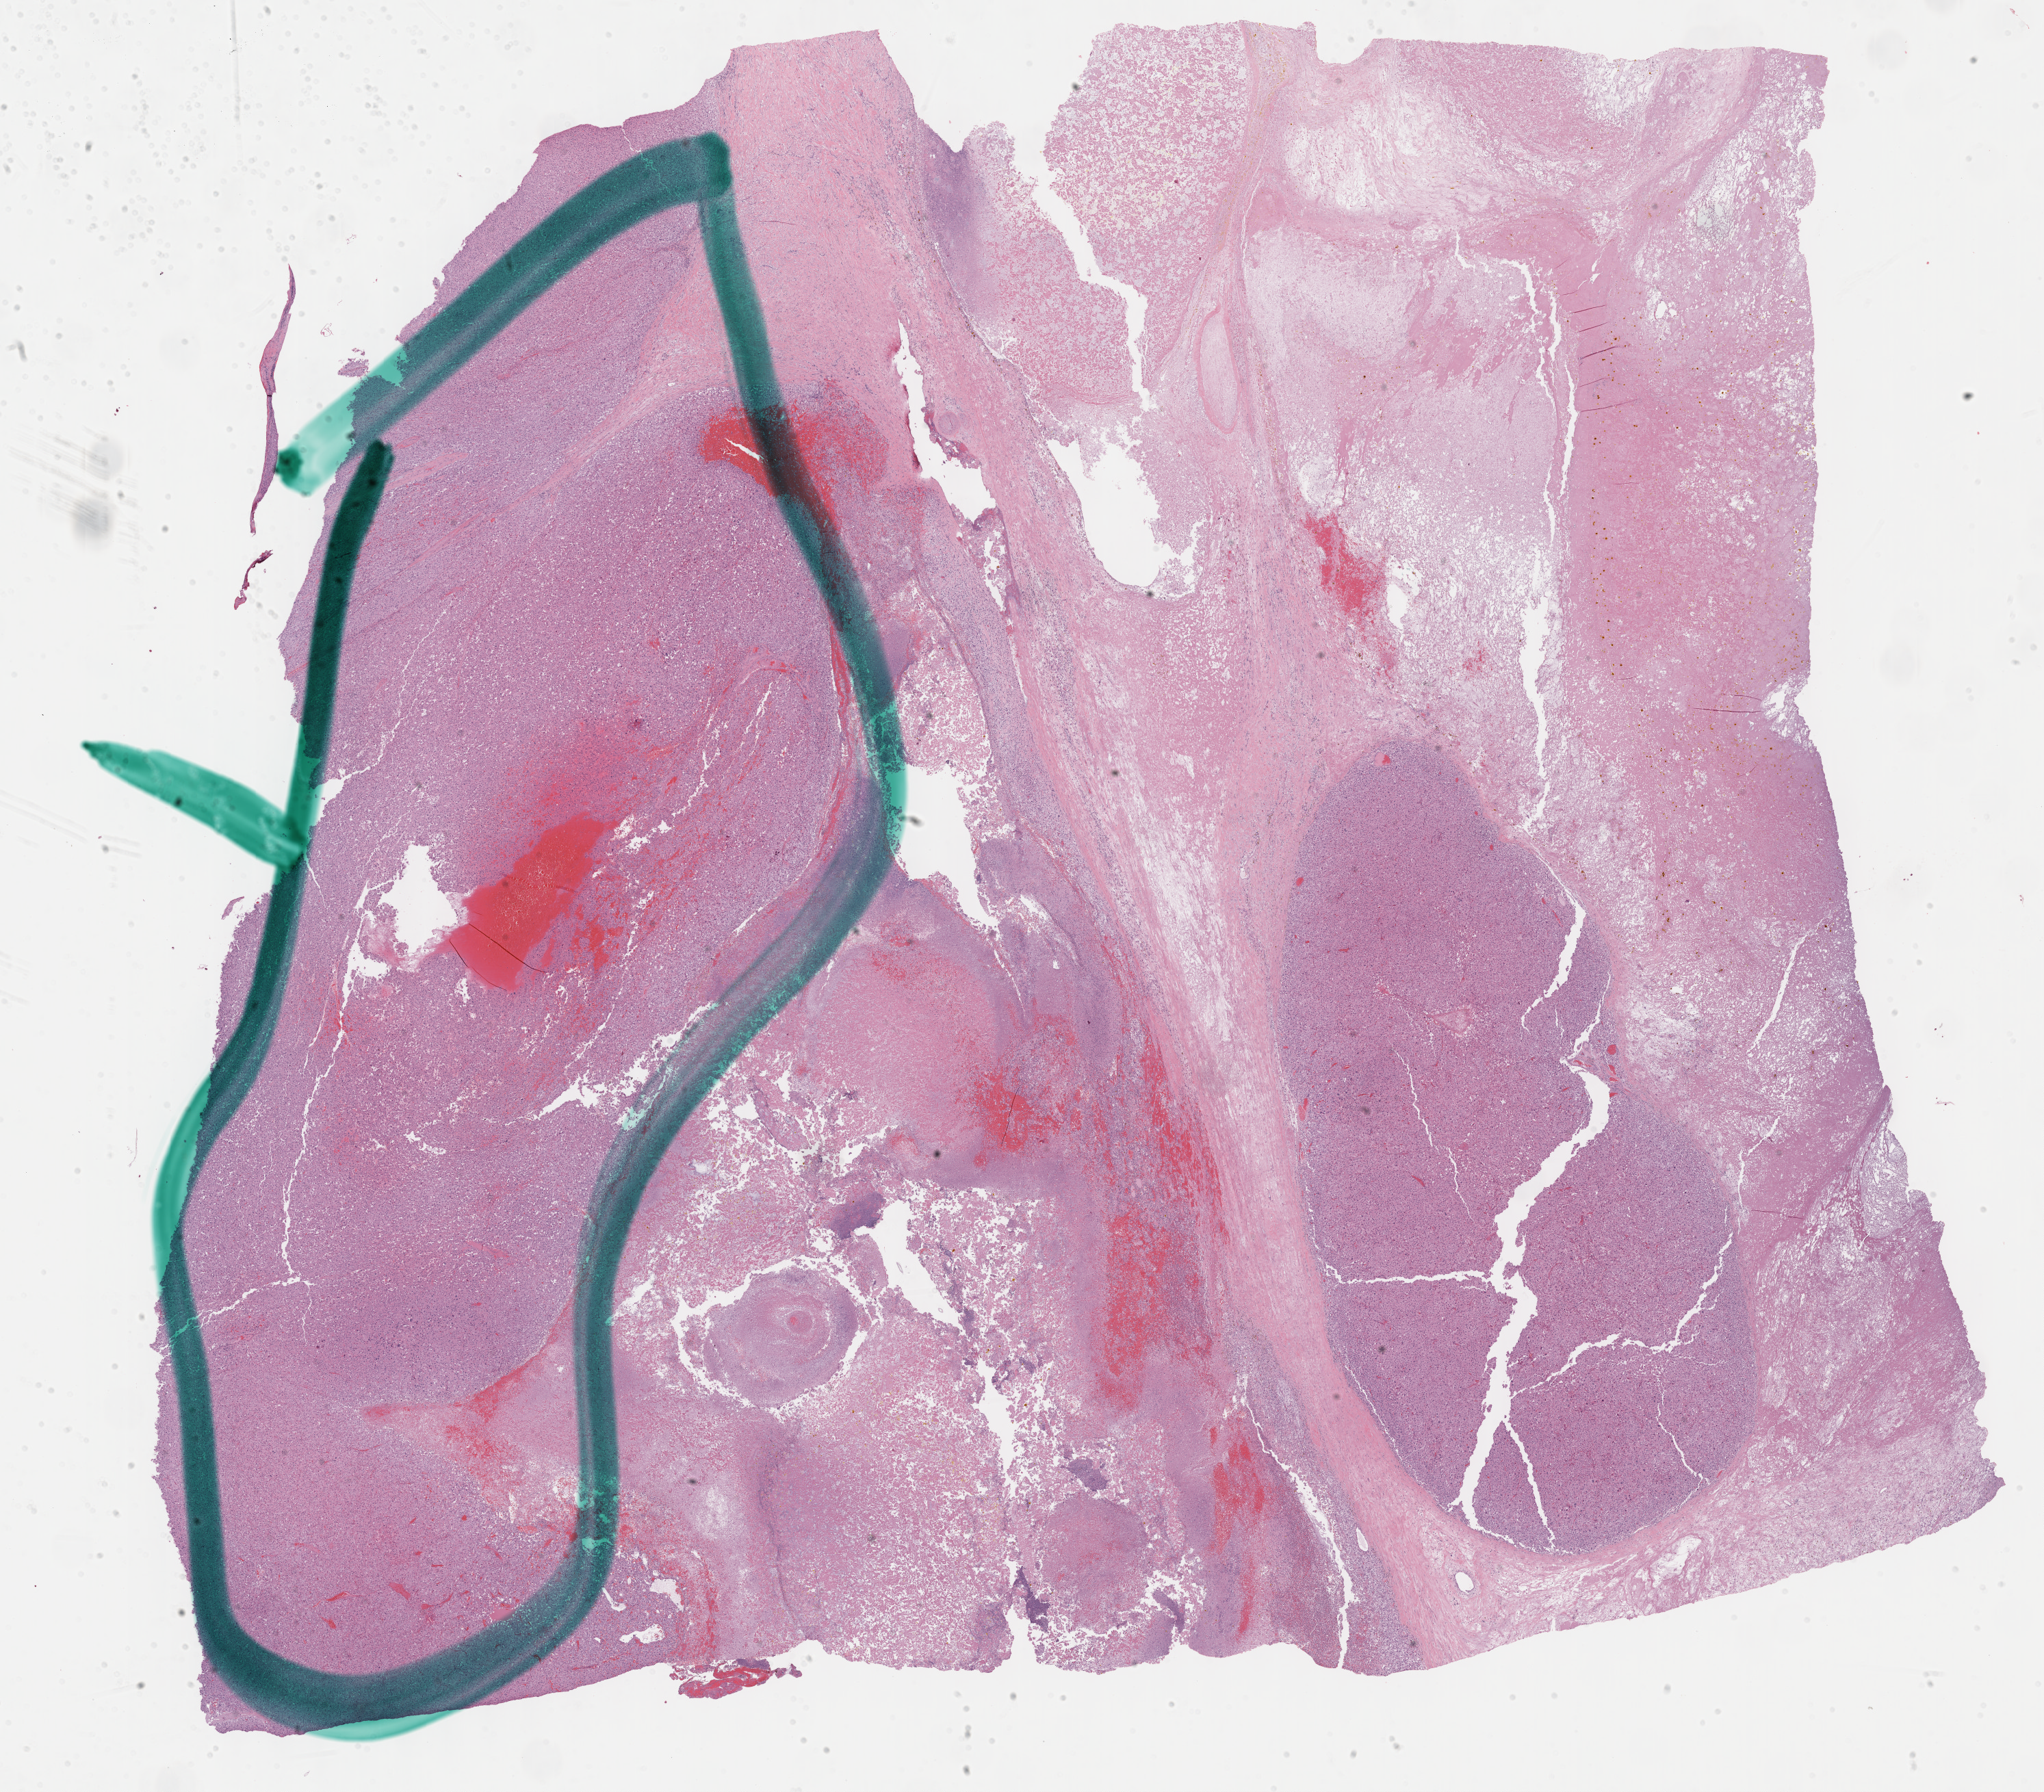
Whole-slide histology image, H&E-stained, shown as a low-resolution overview of the whole scanned area (about 24.2 x 21.2 mm); FFPE section; primary tumour sample from the adrenal cortex. Female patient; age at initial diagnosis 65 years.
Lymph nodes positive (case pathology): 0 of 17 examined. Histologic diagnosis: Adrenal cortical carcinoma (cortex of adrenal gland).